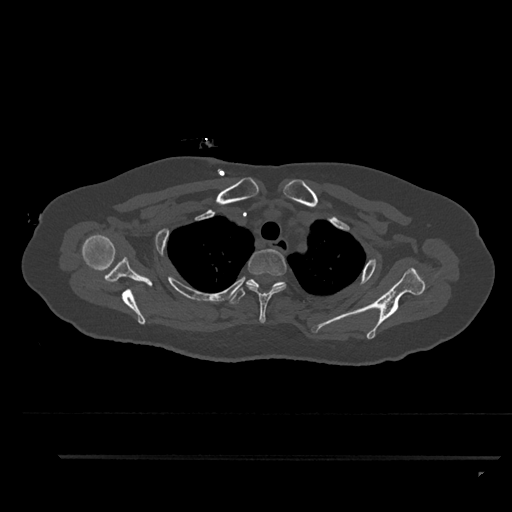
CT including the spine, one axial slice. Reconstruction kernel Br40s/3. 120 kVp. Bone window (W 1800 / L 400 HU). 0.5 mm slice thickness. 512 × 512 image matrix, field of view 408 × 408 mm. Female patient, age 44 years. Case-level facts recorded for this patient, not image findings: primary cancer: renal; vertebrae with lytic lesions (as recorded): L1.
Structures marked on this image (semi-automatic segmentation, software-assisted and operator-edited):
- T1 vertebra: bounding box (x1, y1, x2, y2) in pixels: (279, 284, 286, 287)
- T2 vertebra: (246, 249, 287, 323)
- T3 vertebra: (229, 279, 286, 304)